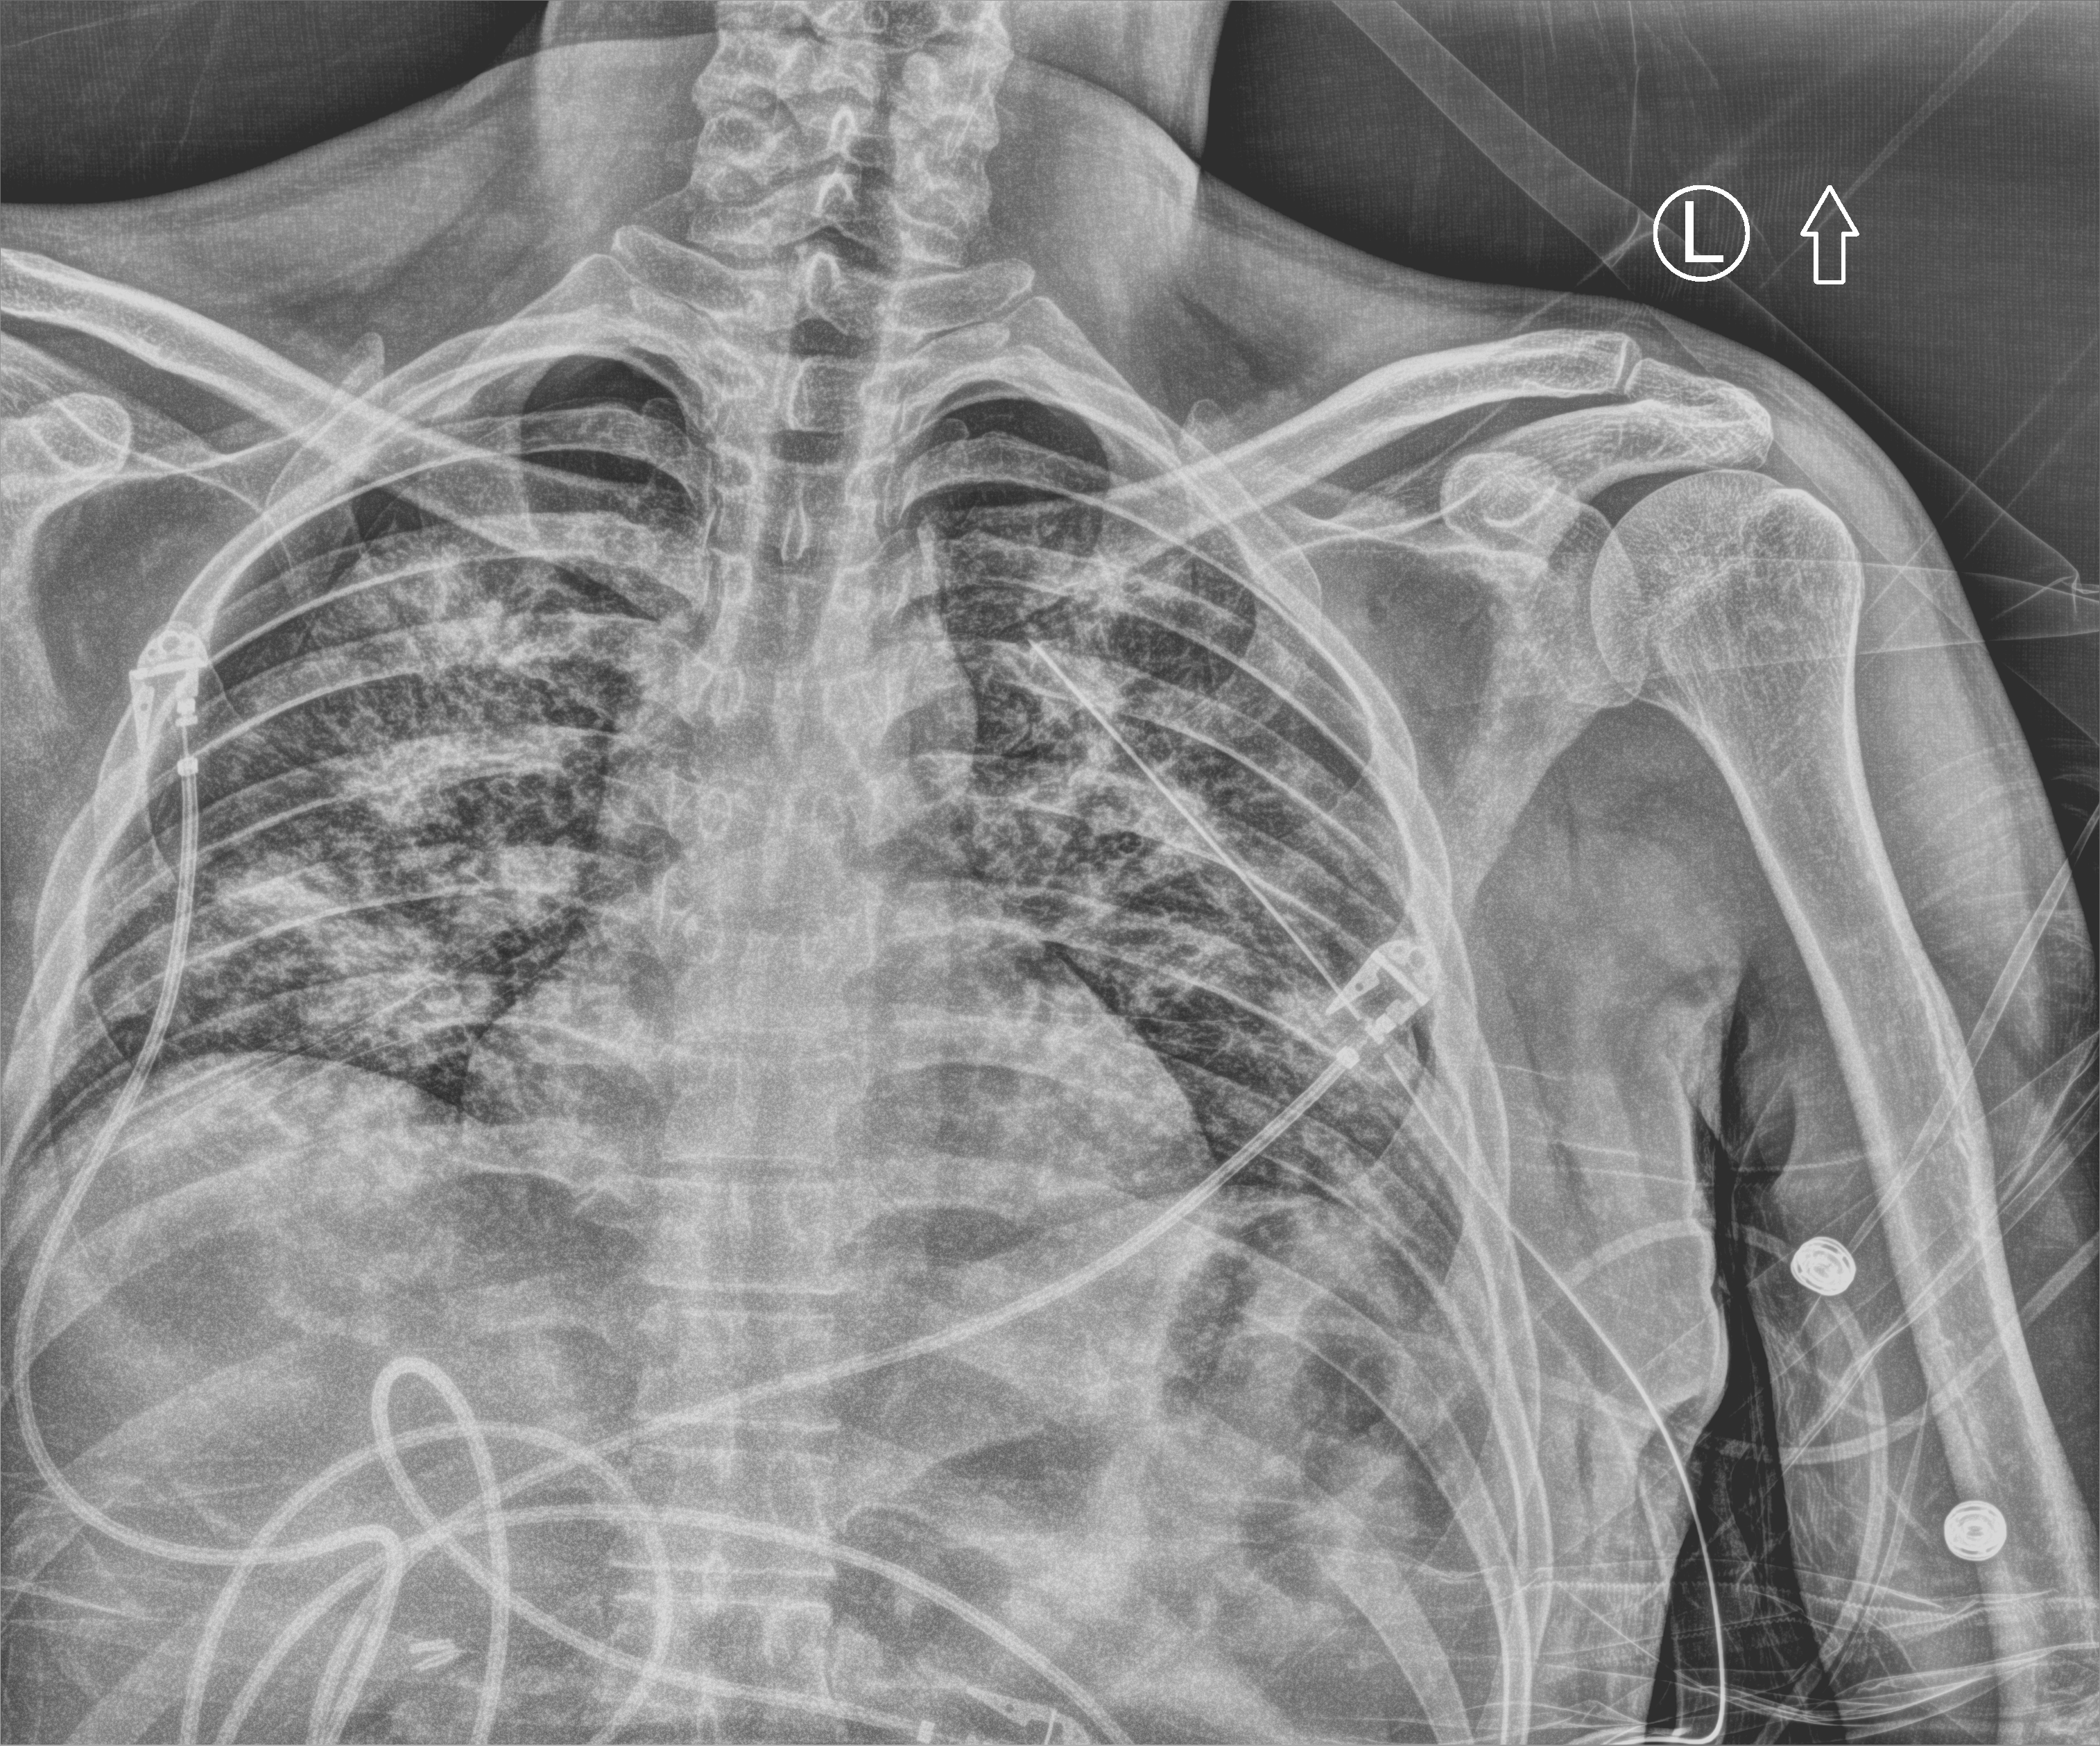
Bedside chest radiograph (computed radiography). Male patient hospitalised with COVID-19, age 18–59 years.
Admission-level facts for this patient (not findings on this image; timing relative to this image not recorded): other chronic lung disease (admission record): no; admitted to intensive care during this hospital stay: yes.